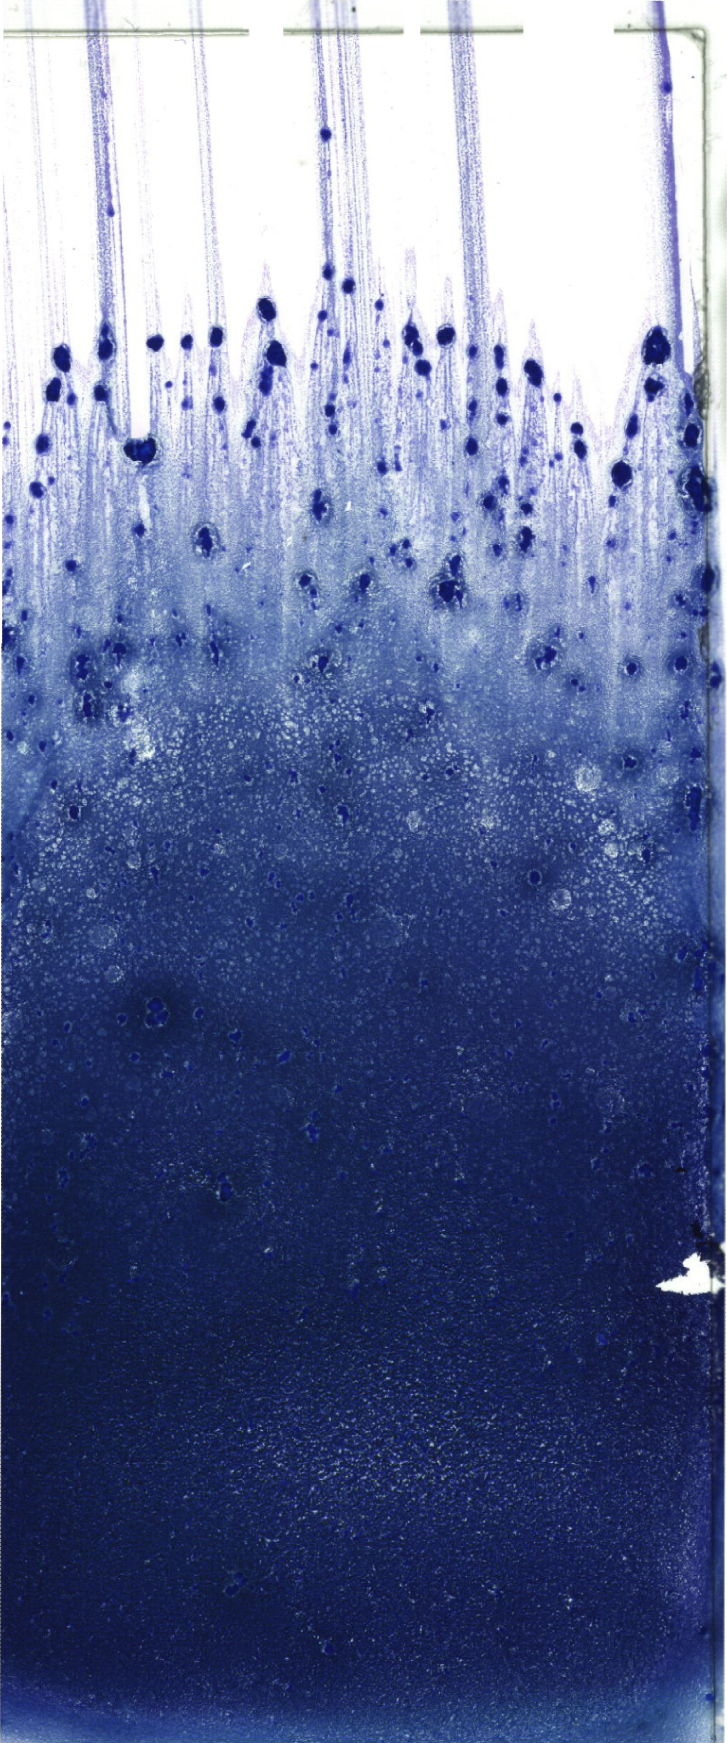
Whole-slide image of a May-Grünwald–Giemsa-stained bone marrow aspirate smear, shown as a low-resolution overview of the whole scanned area (about 20.6 x 49.4 mm). Patient sex: male.
Diagnosis: B Acute Lymphoblastic Leukemia.